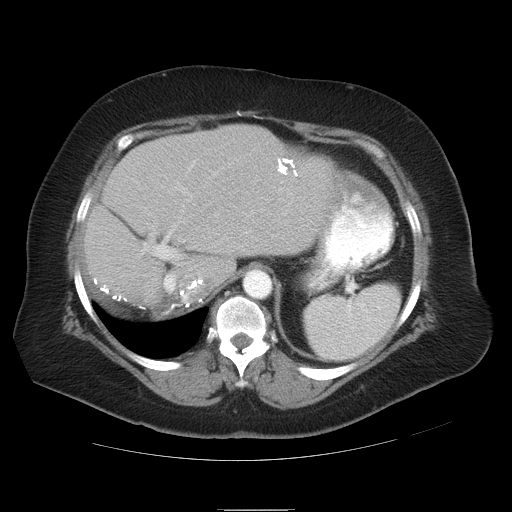
Contrast-enhanced abdominal CT, one axial slice. Slice 26 of 37 in the series (ordered by position). Reconstruction kernel STANDARD. 120 kVp. Intravenous contrast given. Soft-tissue window (W 400 / L 40 HU). 7.5 mm slice thickness. 512 × 512 image matrix, field of view 422 × 422 mm. Female patient, age 68 years. From the clinical record (not read from this slice): diagnosis: colorectal cancer liver metastases, imaged before liver resection; multiple liver metastases: no.
Annotated regions visible in this slice (outlined manually by an expert reader):
- liver: bounding box <86,125,349,306> (left, top, right, bottom; pixels)
- planned liver remnant (the part of the liver to remain after resection): <93,125,349,302>
- portal vein (with intrahepatic branches): <141,166,221,304>